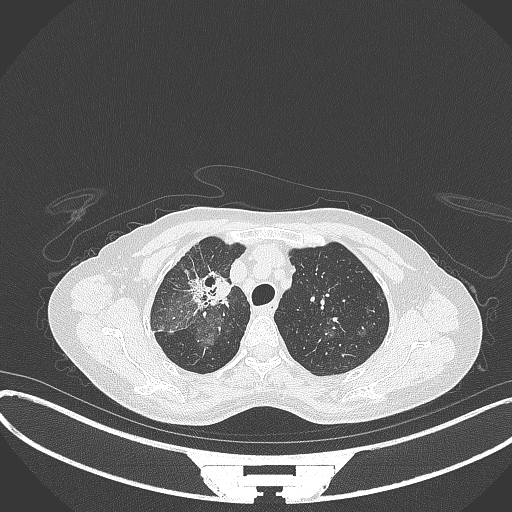
Chest CT, one axial slice. Slice 251 of 284 in the series (ordered by position). Lung window (W 1500 / L -600 HU). 512 × 512 image matrix. Female patient, age 59 years. Case-level facts recorded for this patient, not image findings: clinical TNM (as recorded): T3 N0 M0.
Annotated regions visible in this slice (rectangle marked by the reading radiologist):
- lung tumour (recorded histology: adenocarcinoma): bounding box [x1, y1, x2, y2] px = [188, 264, 232, 309]